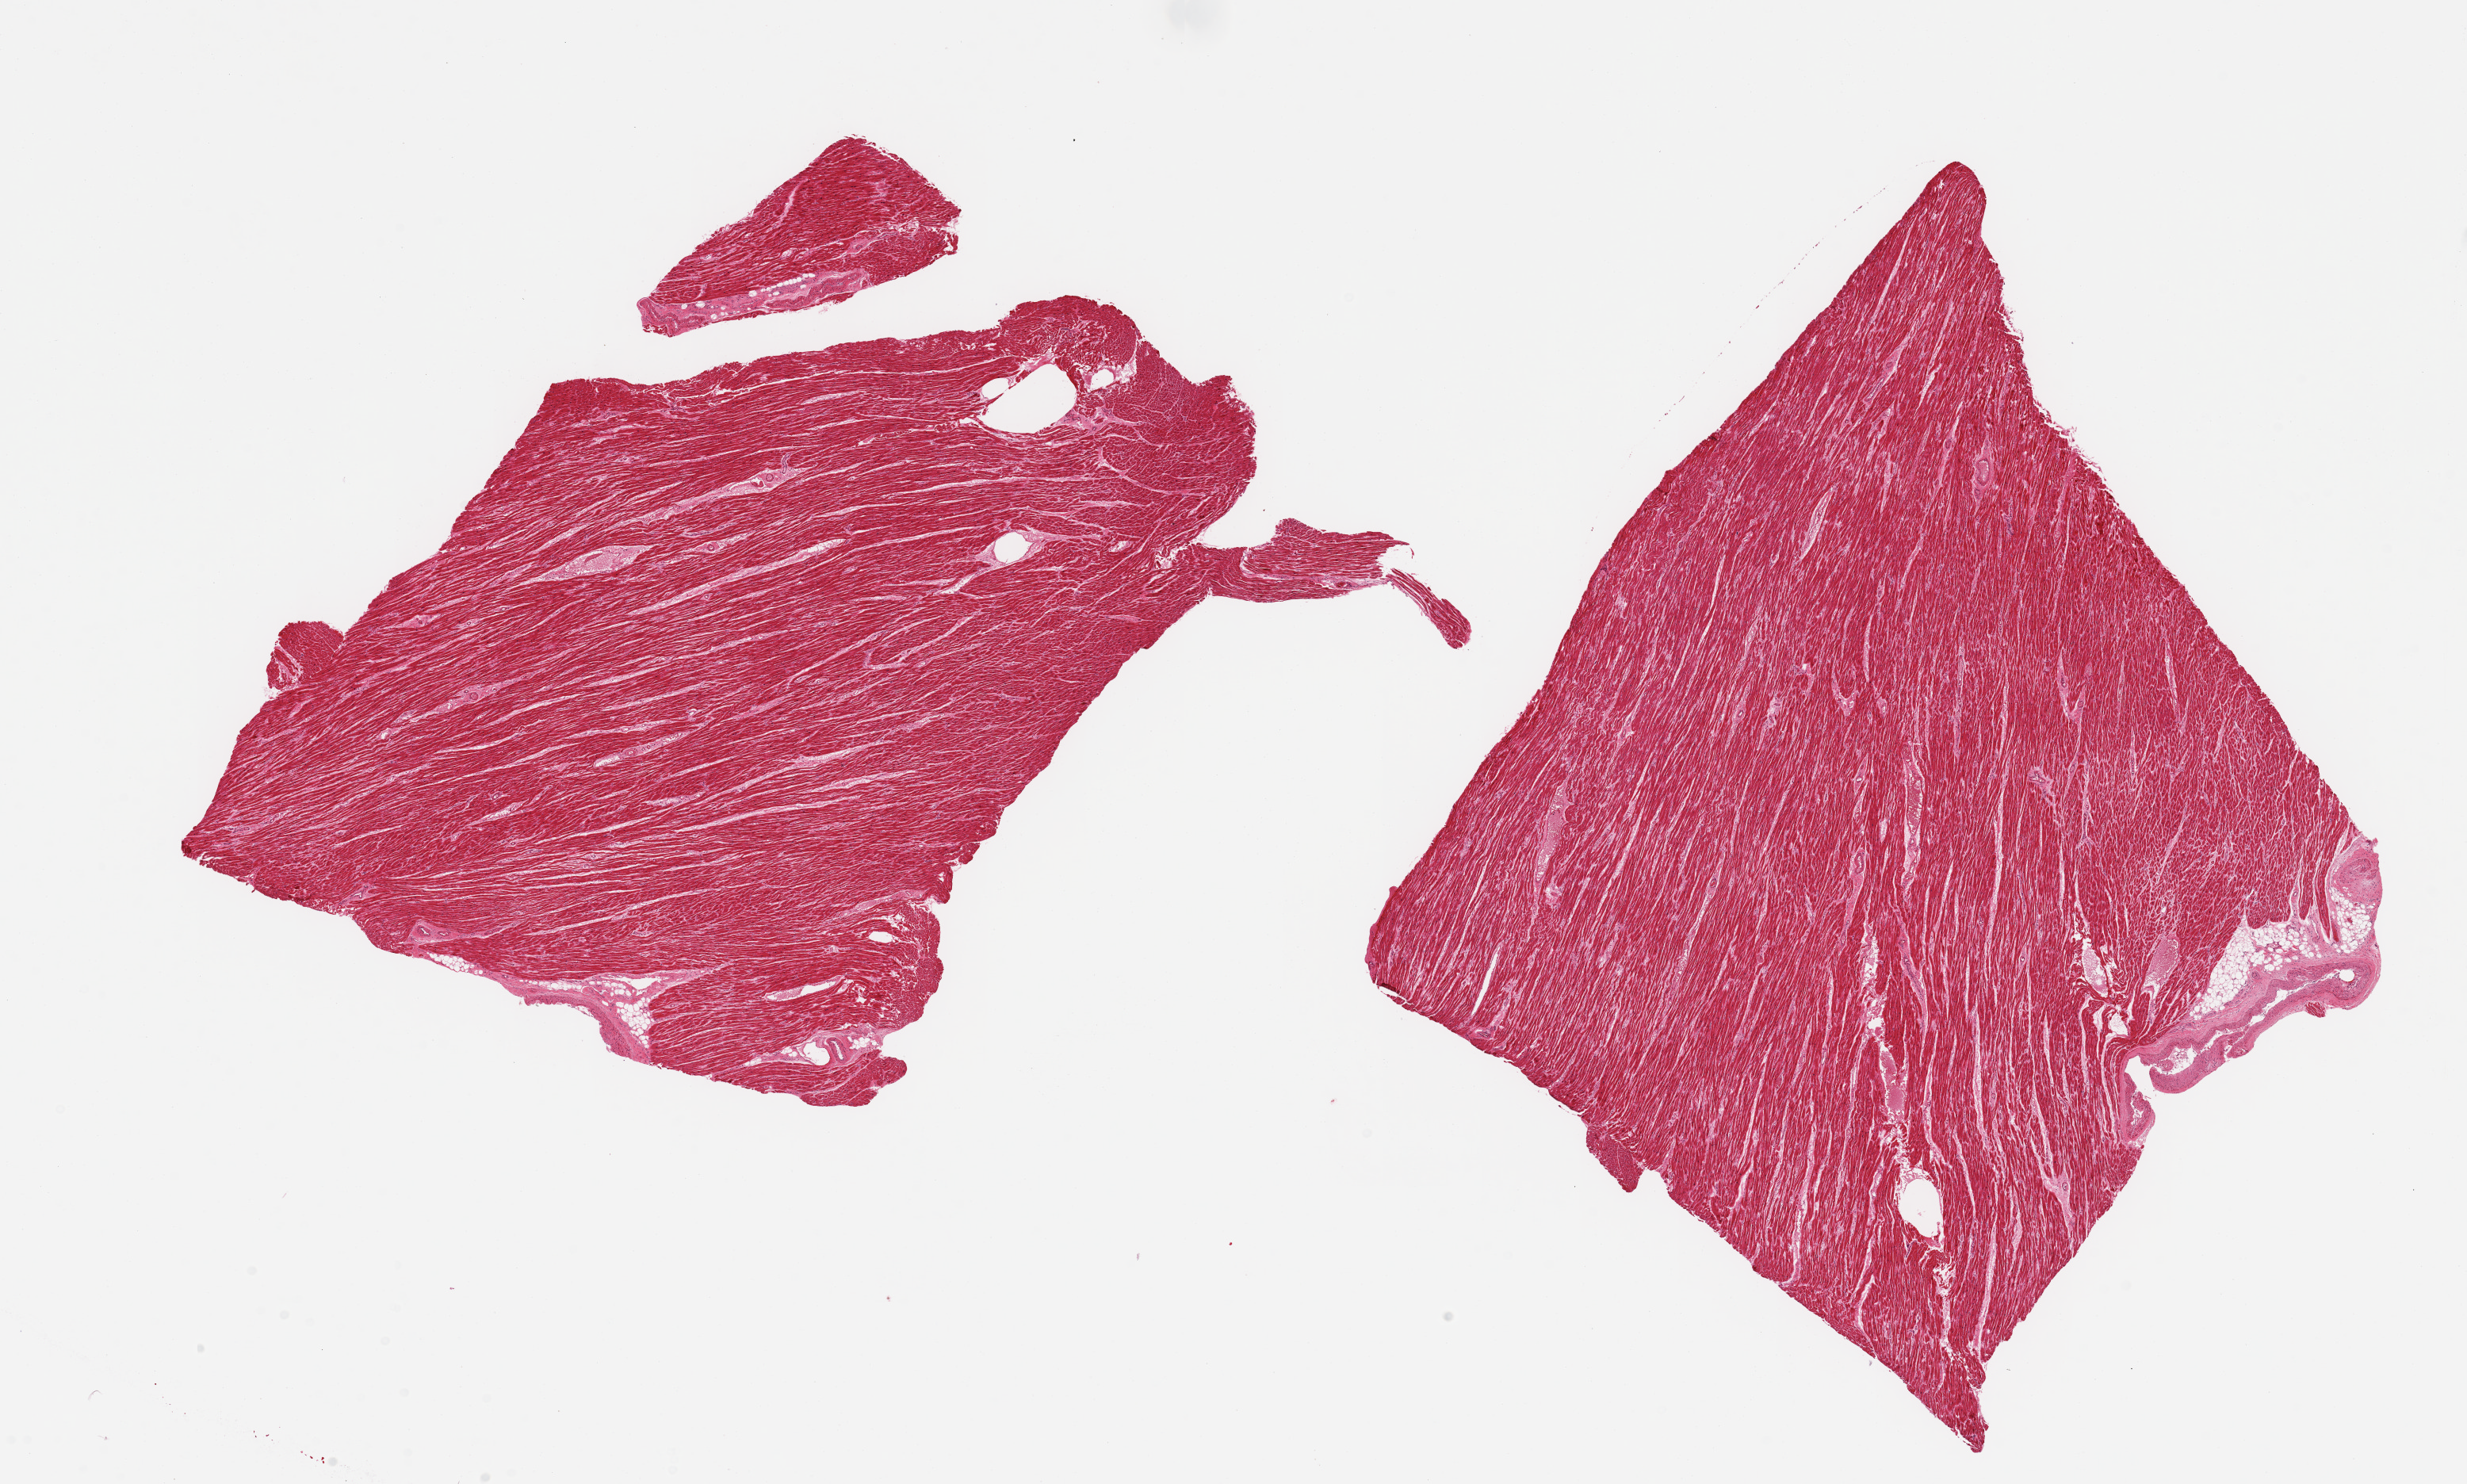
Hematoxylin and eosin (H&E) whole-slide image, whole scanned area (about 24.6 x 14.8 mm, acquisition: 20x scan) shown as a low-resolution overview, PAXgene-fixed paraffin-embedded (PFPE) section, sampled site (target tissue): heart, donor tissue sample. Donor sex: male.
* reviewer comment on this tissue sample: 2 pieces, minimal chronic ischemic changes, interstitial fibrosis